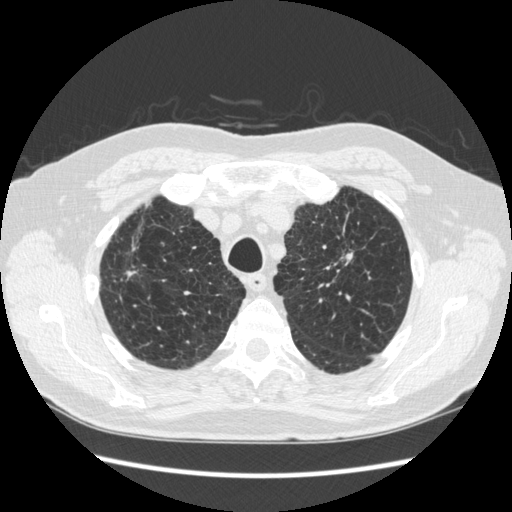
Low-dose screening chest CT, one axial slice. Position 218 of 267 along the scan axis. Reconstruction kernel STANDARD. 120 kVp. Lung window (W 1500 / L -600 HU). 512 × 512 image matrix, field of view 360 × 360 mm.
Outlined on this slice (expert manual segmentation):
- lesion 1 (tumor, upper lobe of left lung): box from (x=335, y=253) to (x=353, y=265) px